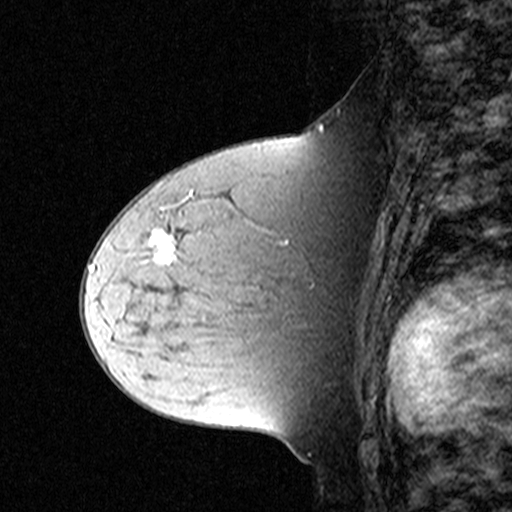
Breast MRI (dynamic contrast-enhanced), one sagittal slice. Position 23 of 44 along the scan axis. Dynamic contrast-enhanced study with each time point stored as its own series, time point 2 of 3 at this slice position (early post-contrast, ordered by acquisition time). 1.5 T. TE 4.5 ms, TR 11 ms. 3 mm slice thickness. 512 × 512 image matrix. Patient: female, 44 years. From the clinical record (not read from this slice): setting: breast cancer imaged before/during neoadjuvant chemotherapy; receptor status: triple-negative.
Structures marked on this image (semi-automatic segmentation, software-assisted and operator-edited):
- analysis volume of interest (the breast-tissue region the enhancement analysis was run in; not a lesion): bounding box [x1, y1, x2, y2] px = [132, 212, 309, 331]
- tumour enhancement mask (voxels above the 90 % enhancement threshold inside the analysis volume of interest): [151, 229, 177, 263]